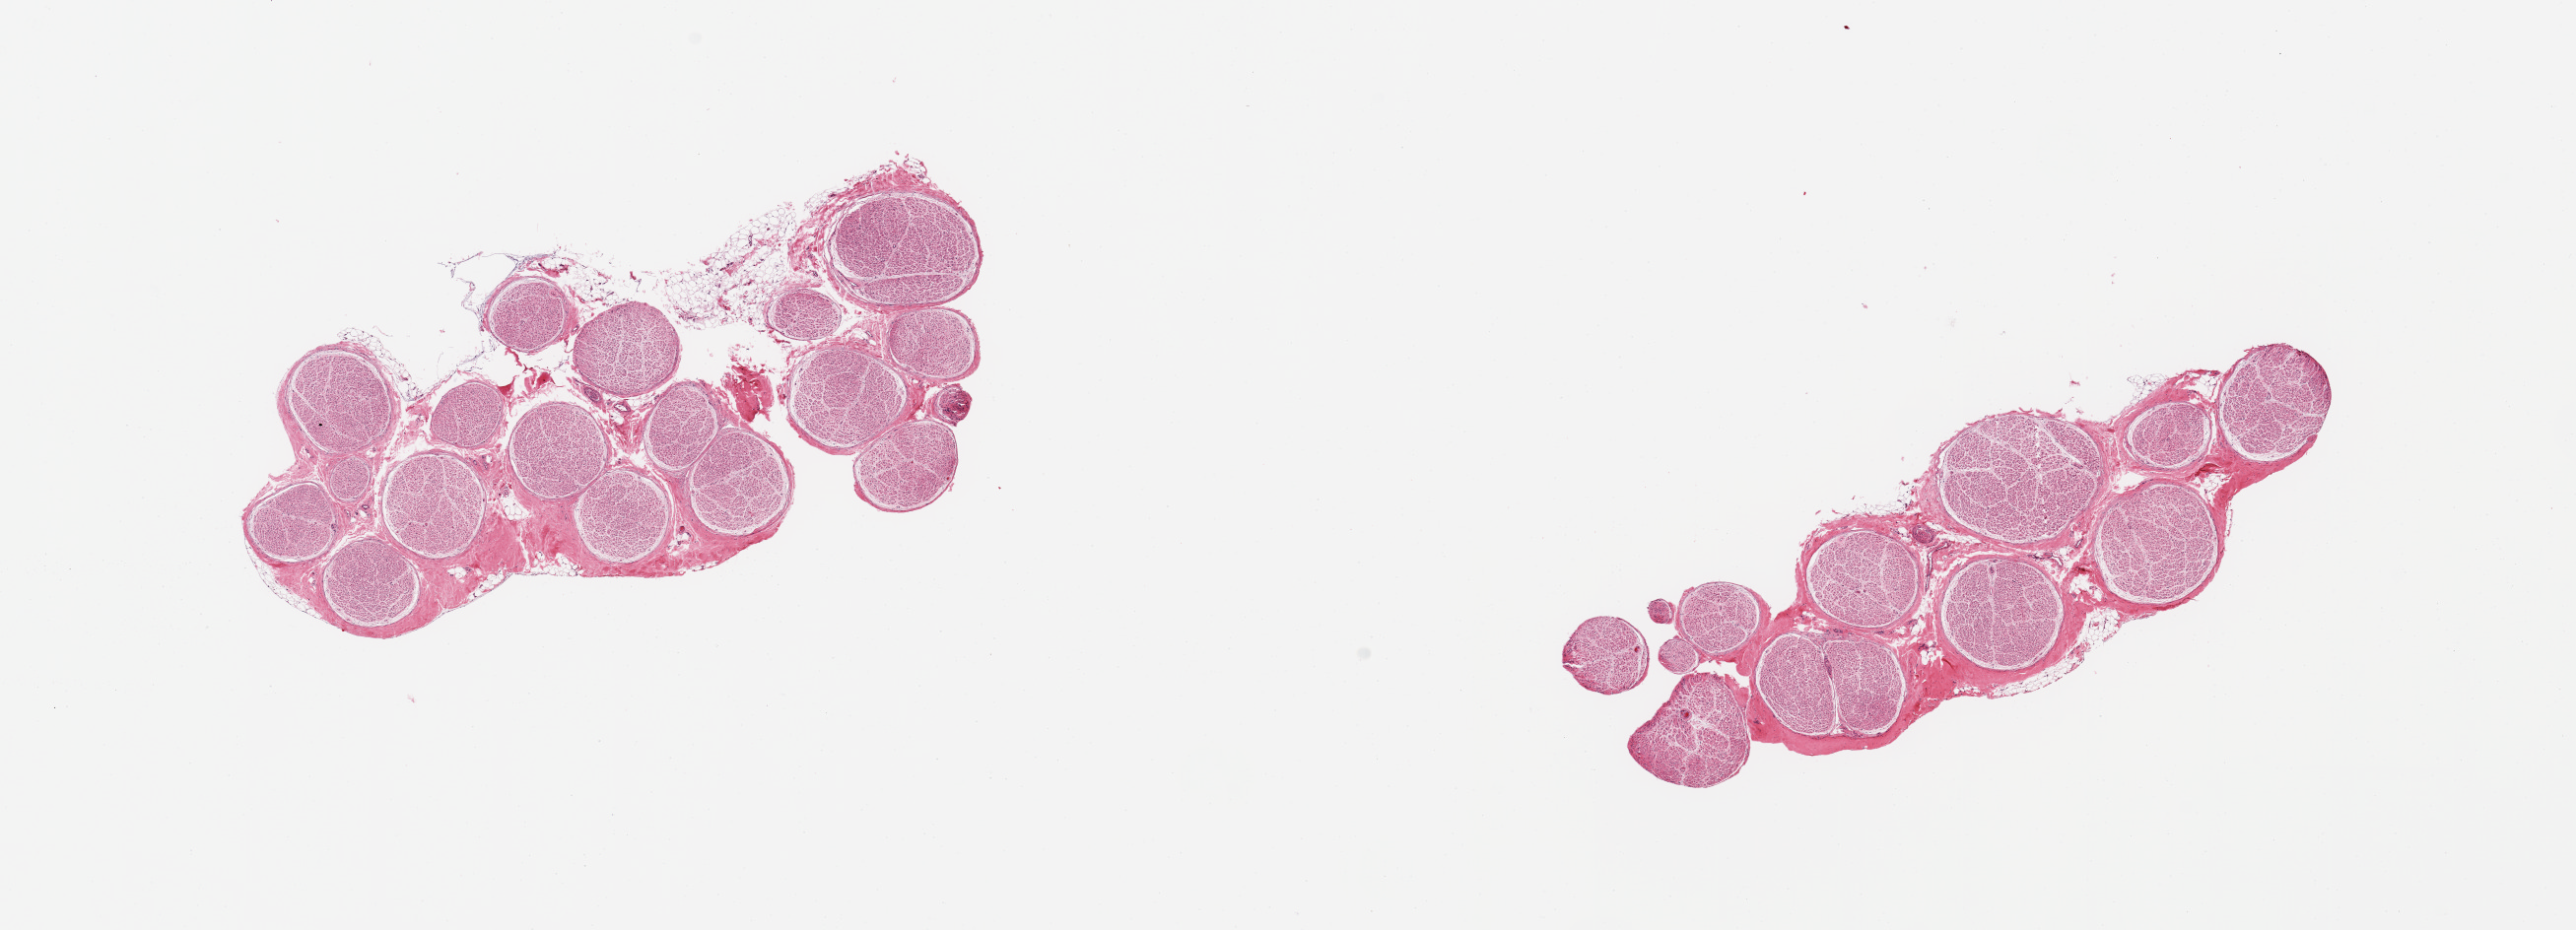
Whole-slide image, H&E stain, brightfield — whole scanned area (about 20.7 x 7.5 mm) shown as a low-resolution overview. PAXgene-fixed paraffin-embedded (PFPE) section. Target tissue: tibial nerve. Donor tissue sample. Male donor.
* review note (as recorded): 2 pieces, minimal adherent fat